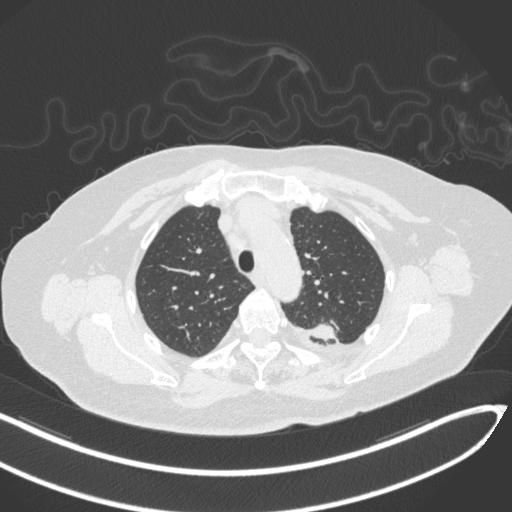
Chest CT, one axial slice. Position 248 of 270 along the scan axis. Reconstruction kernel B31f. Lung window (W 1500 / L -600 HU). 1 mm slice thickness. 512 × 512 image matrix, field of view 400 × 400 mm. Female patient, age 76 years. From the clinical record (not read from this slice): clinical TNM (as recorded): T1c N0 M0.
Structures marked on this image (rectangle marked by the reading radiologist):
- lung tumour (recorded histology: adenocarcinoma): bounding box [x1, y1, x2, y2] px = [305, 319, 340, 343]